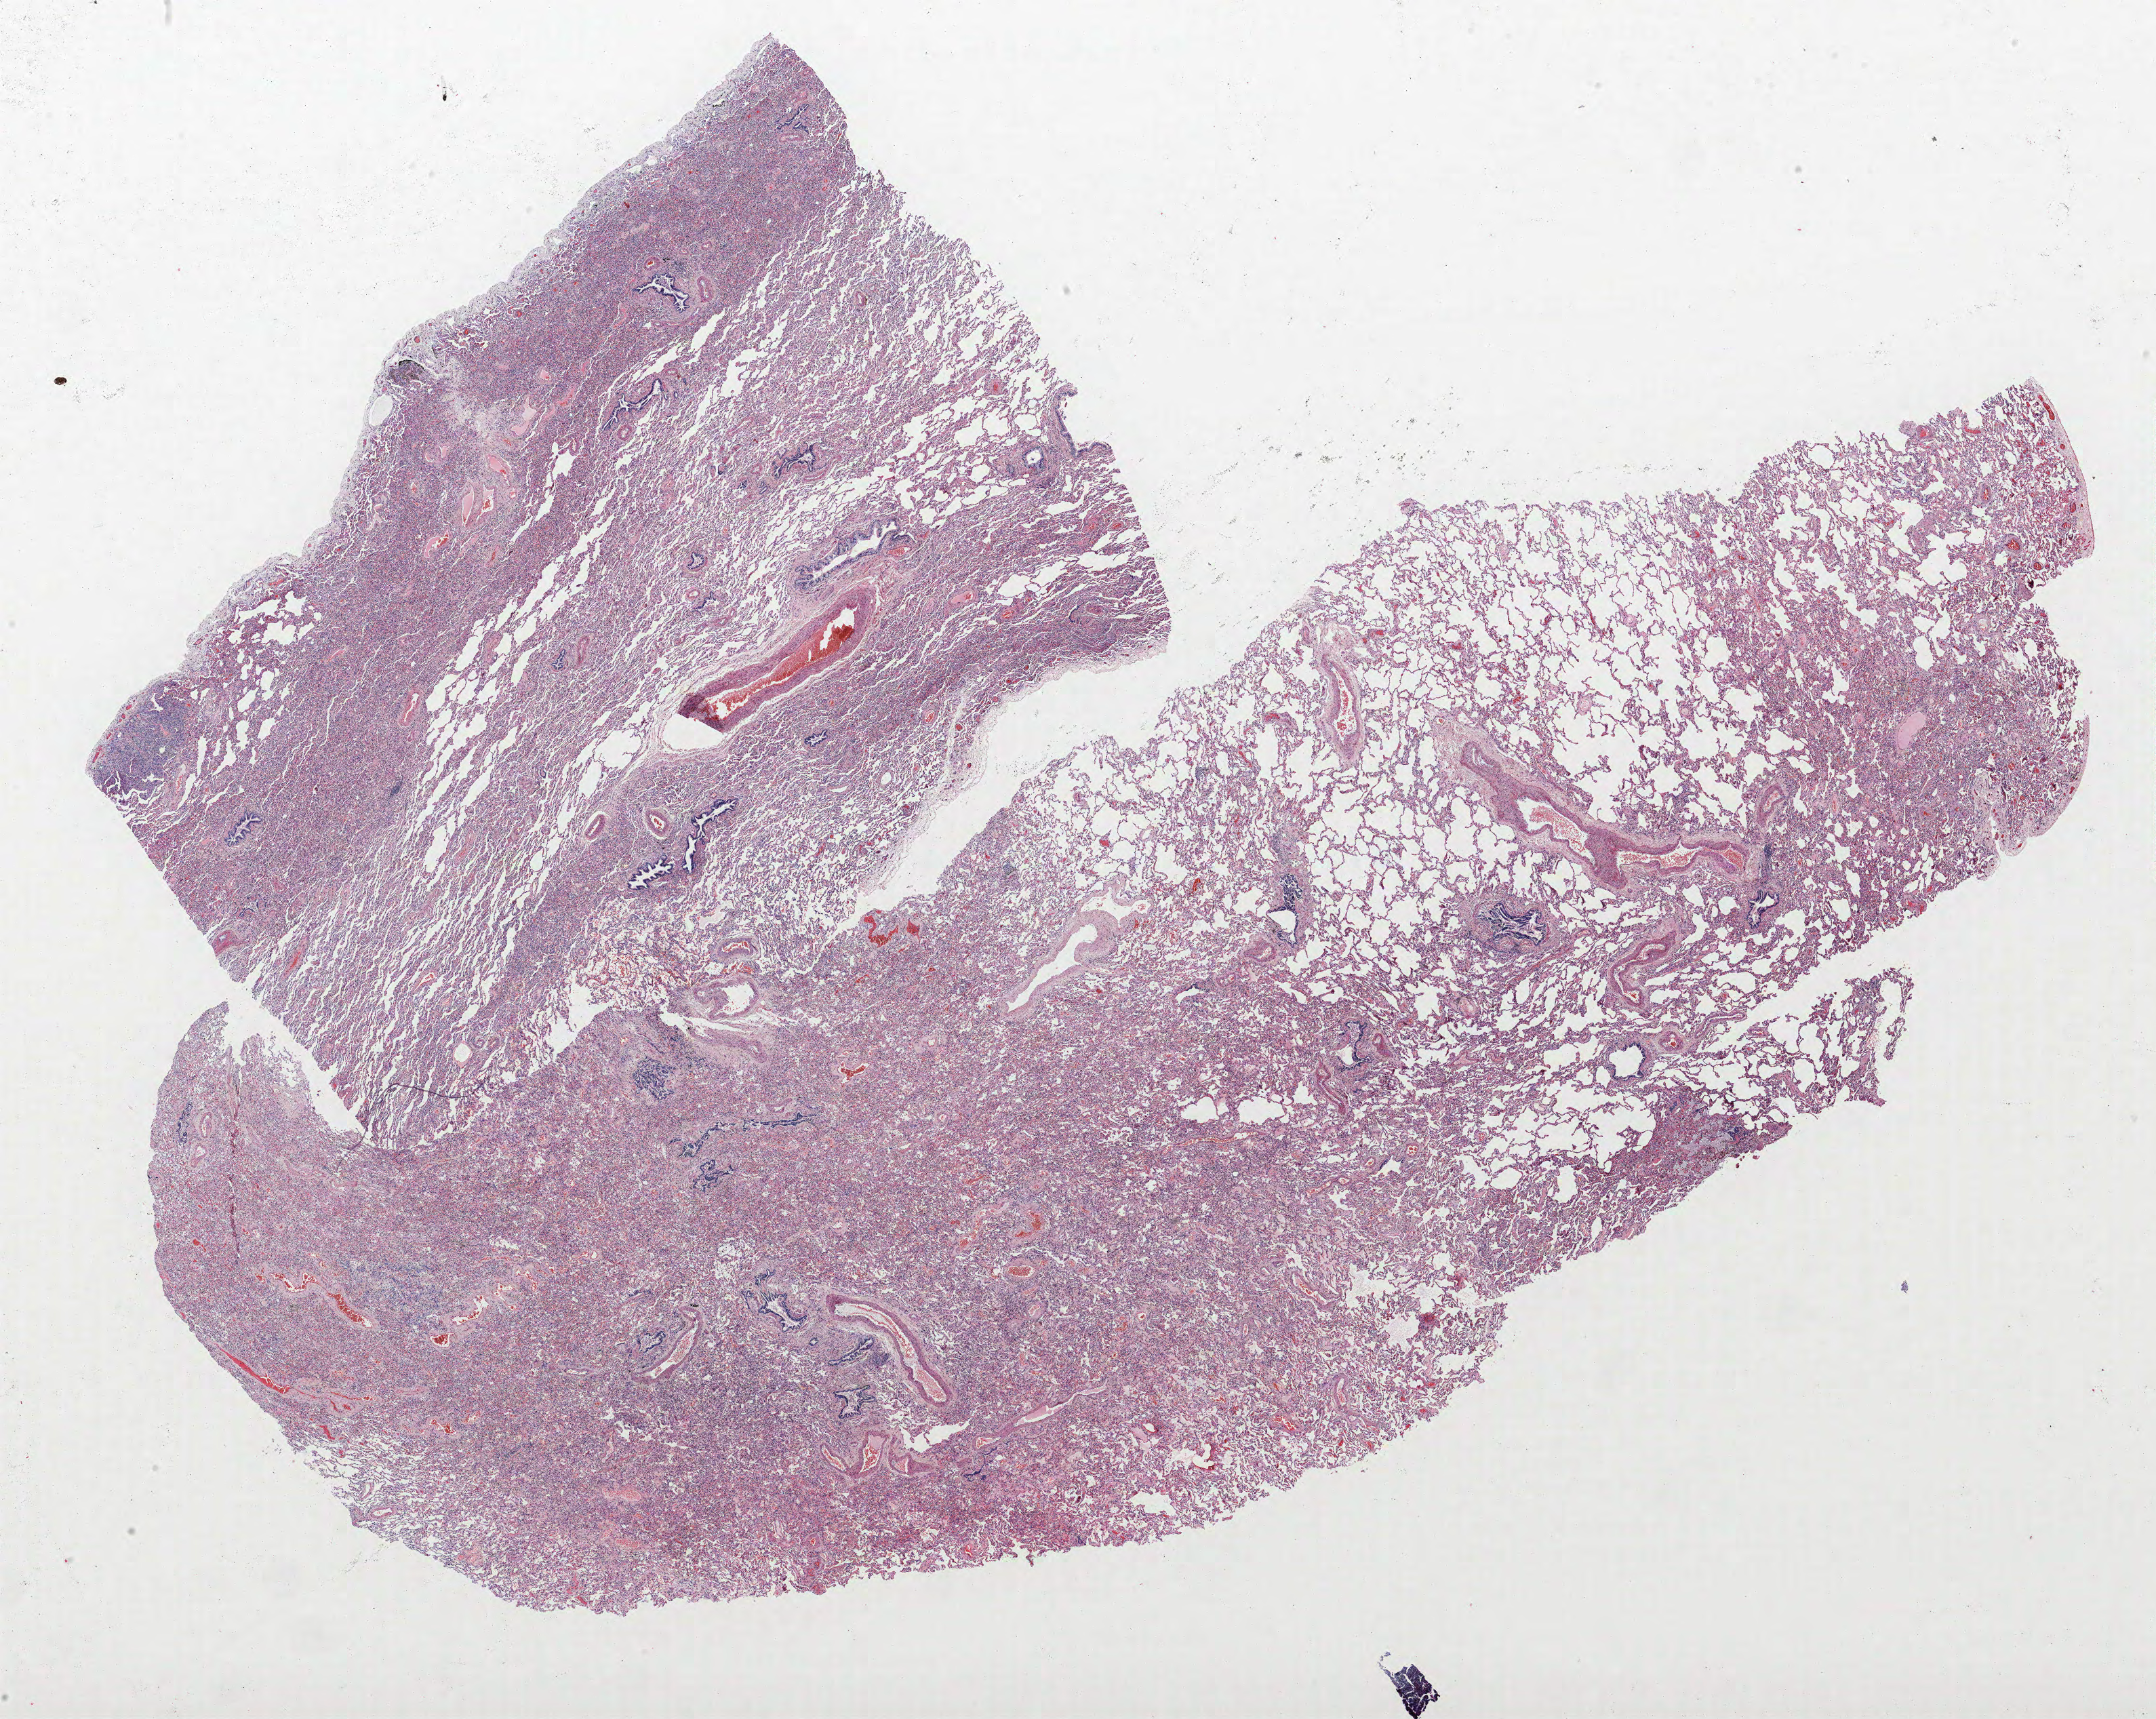
Whole-slide histology image, Hematoxylin and eosin (H&E) stained — low-resolution overview of the scanned area, about 25.4 x 20.3 mm. Formalin-fixed paraffin-embedded (FFPE) section. Lung. Female, age 60 at enrolment.
* tumour size (pathology): 15 mm
* stage (AJCC 6th edition): IA
* participant's lung-cancer diagnosis: Bronchiolo-alveolar carcinoma, non-mucinous (ICD-O-3 8252/3)
* primary tumour location (clinical record): right lower lobe